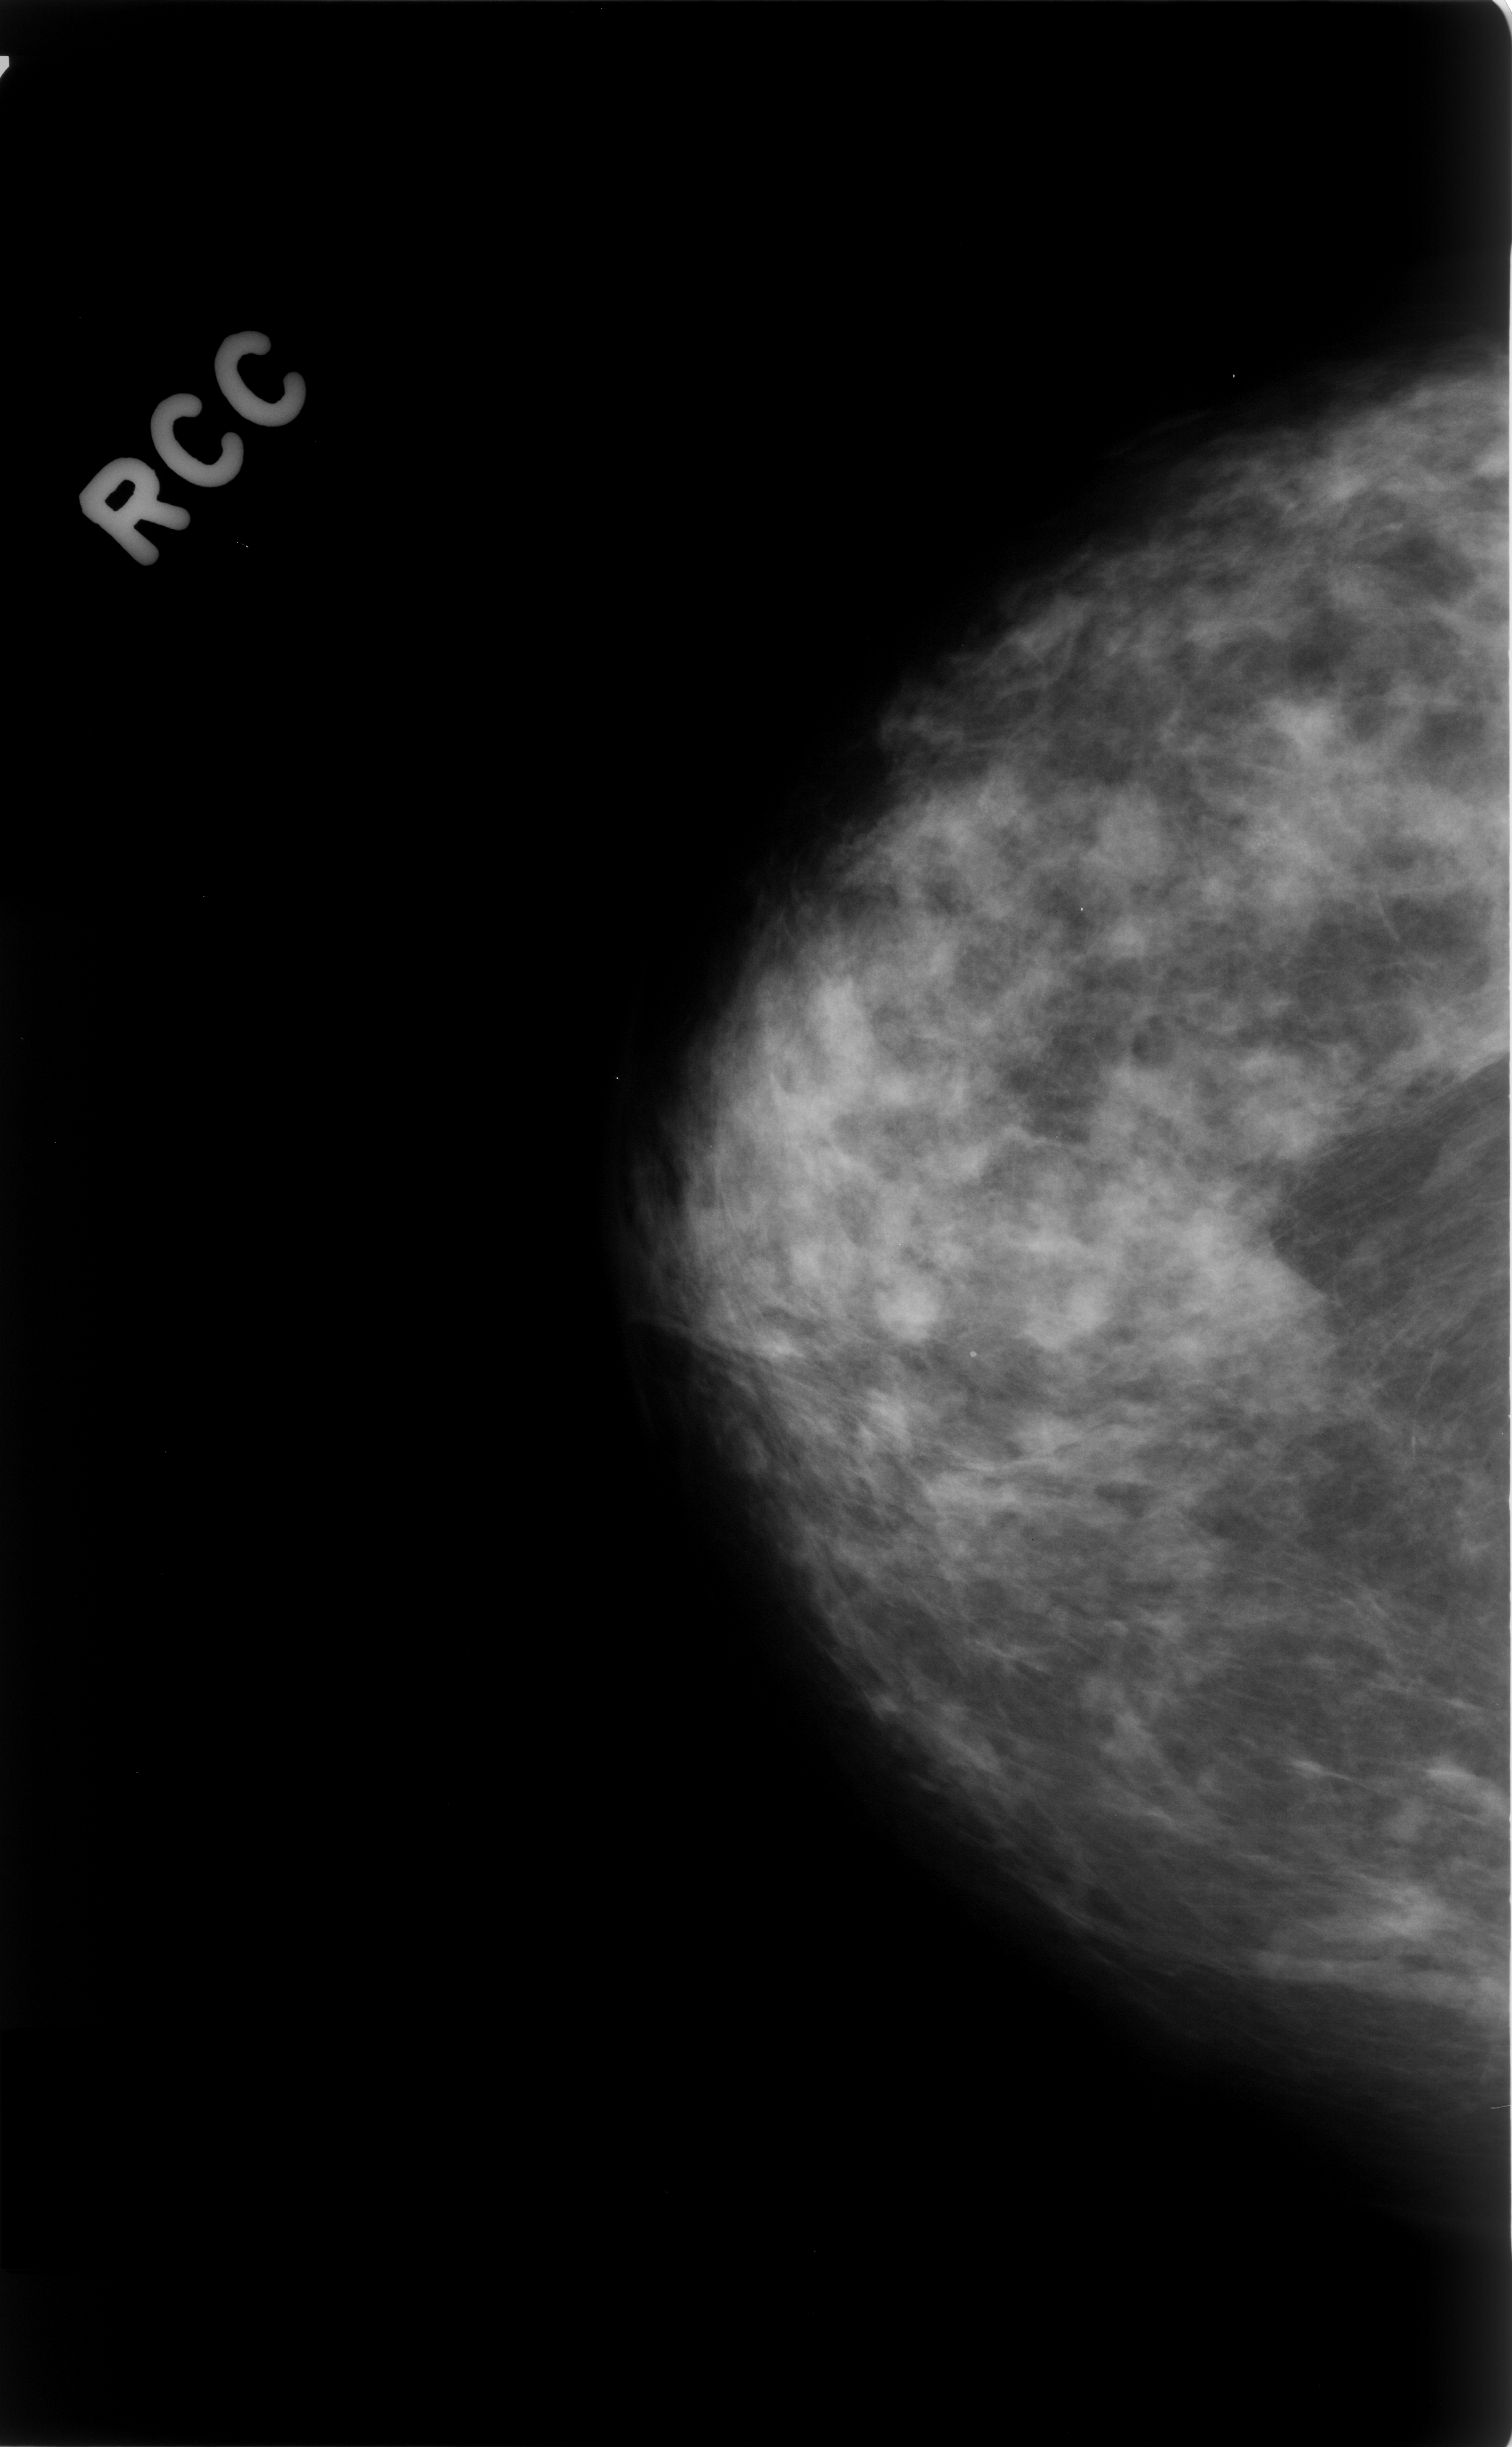
Scanned film-screen mammogram; right breast; craniocaudal (CC) view; BI-RADS breast density category 2 (scale 1–4); 1512 × 2447 image matrix.
Expert-marked regions of interest on this film, with their recorded descriptors:
- calcifications, morphology amorphous, distribution clustered; BI-RADS assessment category 4; subtlety rating 2 on a 1 (subtle) to 5 (obvious) scale; pathology result (as recorded, not read from the image): benign: bounding box [x1, y1, x2, y2] px = [1150, 671, 1411, 982]